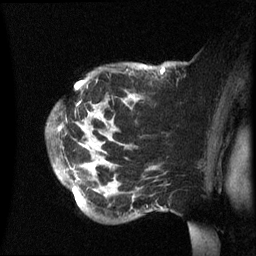
Breast MRI (dynamic contrast-enhanced), one sagittal slice. Slice 45 of 60 in the series (ordered by position). Dynamic contrast-enhanced series, image 2 of 3 at this slice position (ordered by acquisition). 1.5 T. TE 4.2 ms, TR 8.4 ms. 256 × 256 image matrix, field of view 230 × 230 mm. Female patient, age 49 years.
Annotated regions visible in this slice (semi-automatically segmented with operator editing):
- analysis volume of interest (the breast-tissue region the enhancement analysis was run in; not a lesion): bounding box (x1, y1, x2, y2) in pixels: (46, 62, 174, 222)
- tumour enhancement mask (voxels above the 70 % enhancement threshold inside the analysis volume of interest): (60, 67, 165, 191)